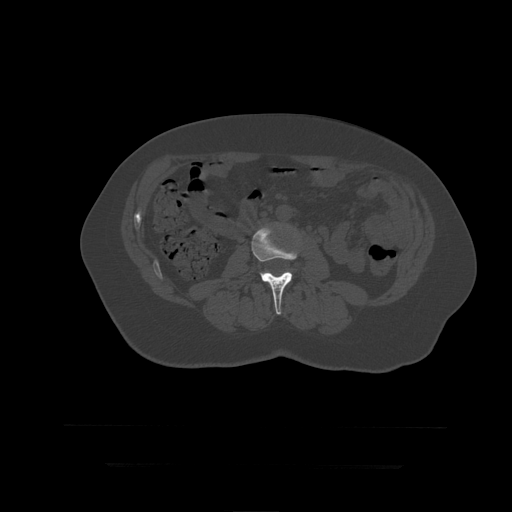
CT including the spine, one axial slice. Reconstruction kernel STANDARD. 120 kVp. Bone window (W 1800 / L 400 HU). 1.25 mm slice thickness. 512 × 512 image matrix, field of view 450 × 450 mm. Patient age 41 years. From the clinical record (not read from this slice): primary cancer: breast.
Outlined on this slice (semi-automatic segmentation, software-assisted and operator-edited):
- L3 vertebra: bounding box (x1, y1, x2, y2) in pixels: (252, 227, 298, 315)